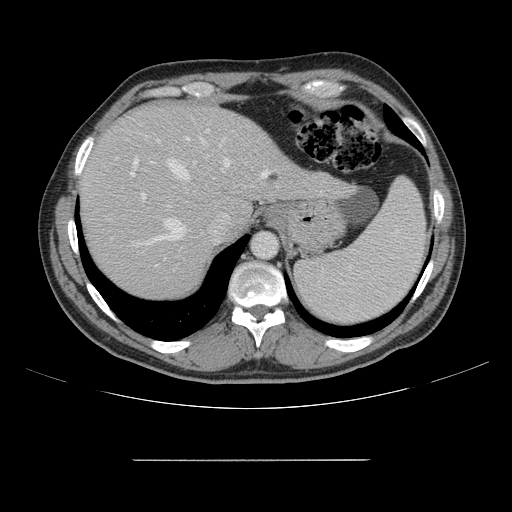
Contrast-enhanced abdominal CT, one axial slice. Position 121 of 164 along the scan axis. 120 kVp. Intravenous contrast given. Soft-tissue window (W 400 / L 40 HU). 2.5 mm slice thickness. 512 × 512 image matrix, field of view 404 × 404 mm. Male patient, age 54 years. From the clinical record (not read from this slice): diagnosis: colorectal cancer liver metastases, imaged before liver resection; multiple liver metastases: yes; largest metastasis: 1 cm; disease in both lobes: no.
Outlined on this slice (outlined manually by an expert reader):
- hepatic veins: bounding box <137,139,269,245> (left, top, right, bottom; pixels)
- liver: <81,105,345,297>
- planned liver remnant (the part of the liver to remain after resection): <81,105,253,297>
- portal vein (with intrahepatic branches): <116,137,223,272>
- liver metastasis: <270,175,279,181>